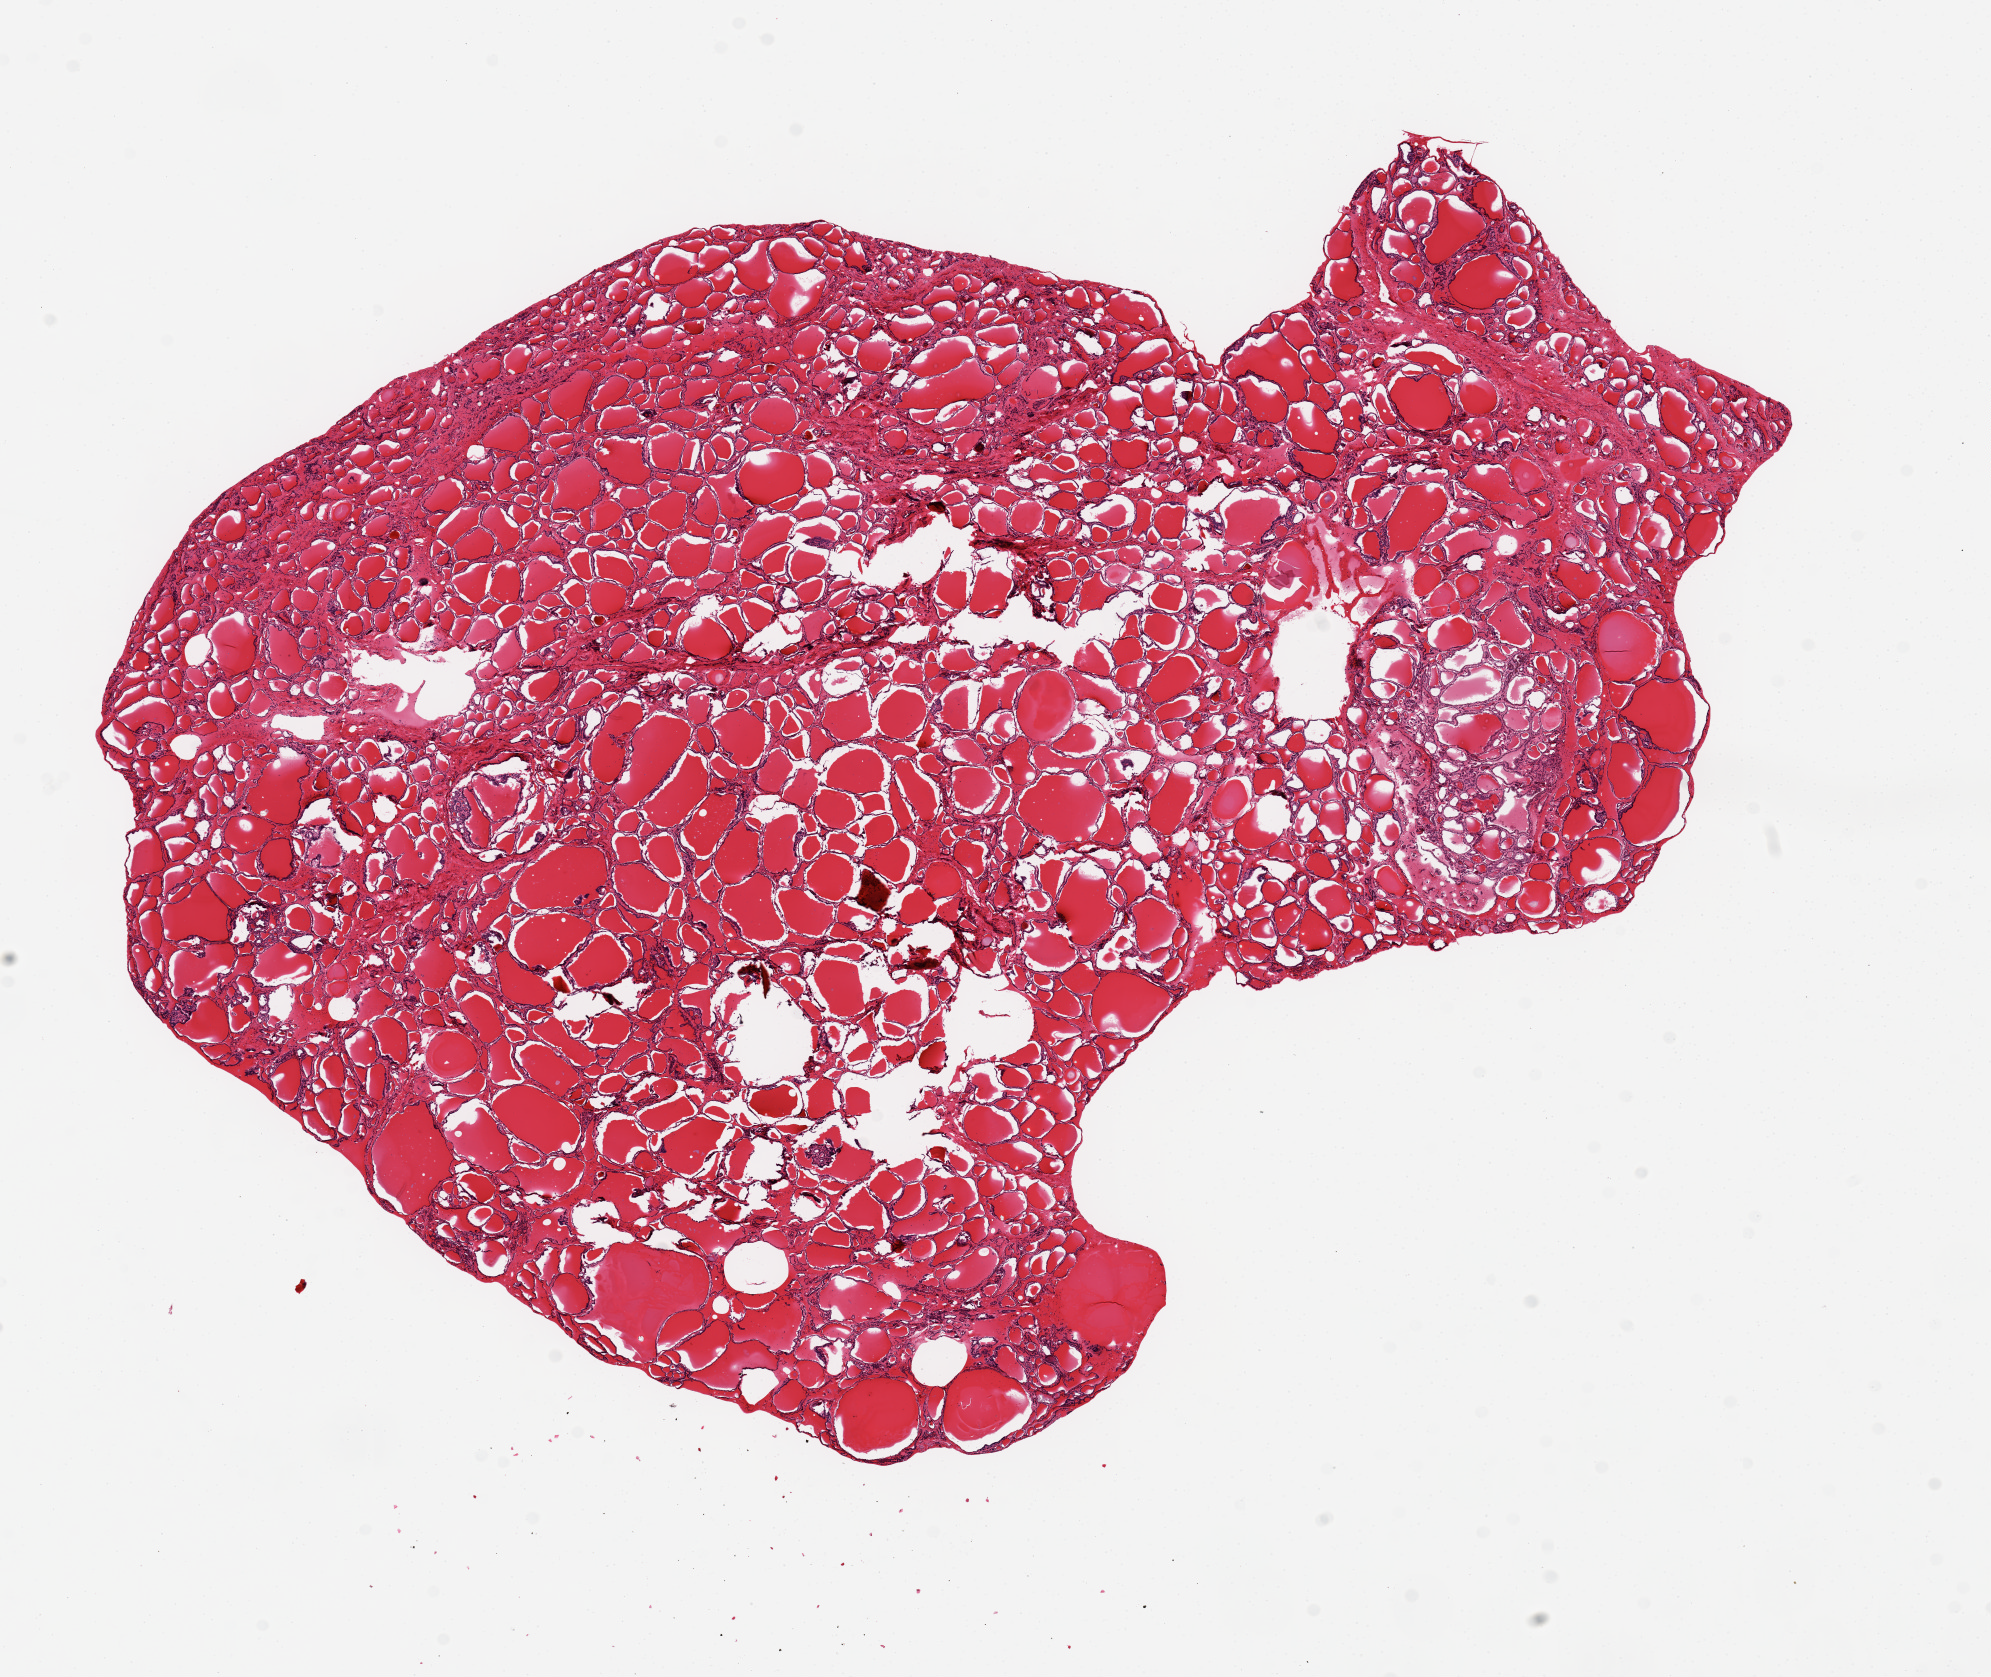
Whole-slide image, H&E stain, brightfield, shown as a low-resolution overview of the whole scanned area (about 15.8 x 13.3 mm); PAXgene-fixed paraffin-embedded (PFPE) section; section of thyroid (target tissue); donor tissue sample. Female donor.
Pathologist's review note for this sample: 1 13x9mm aliquot. Good clean specimen.